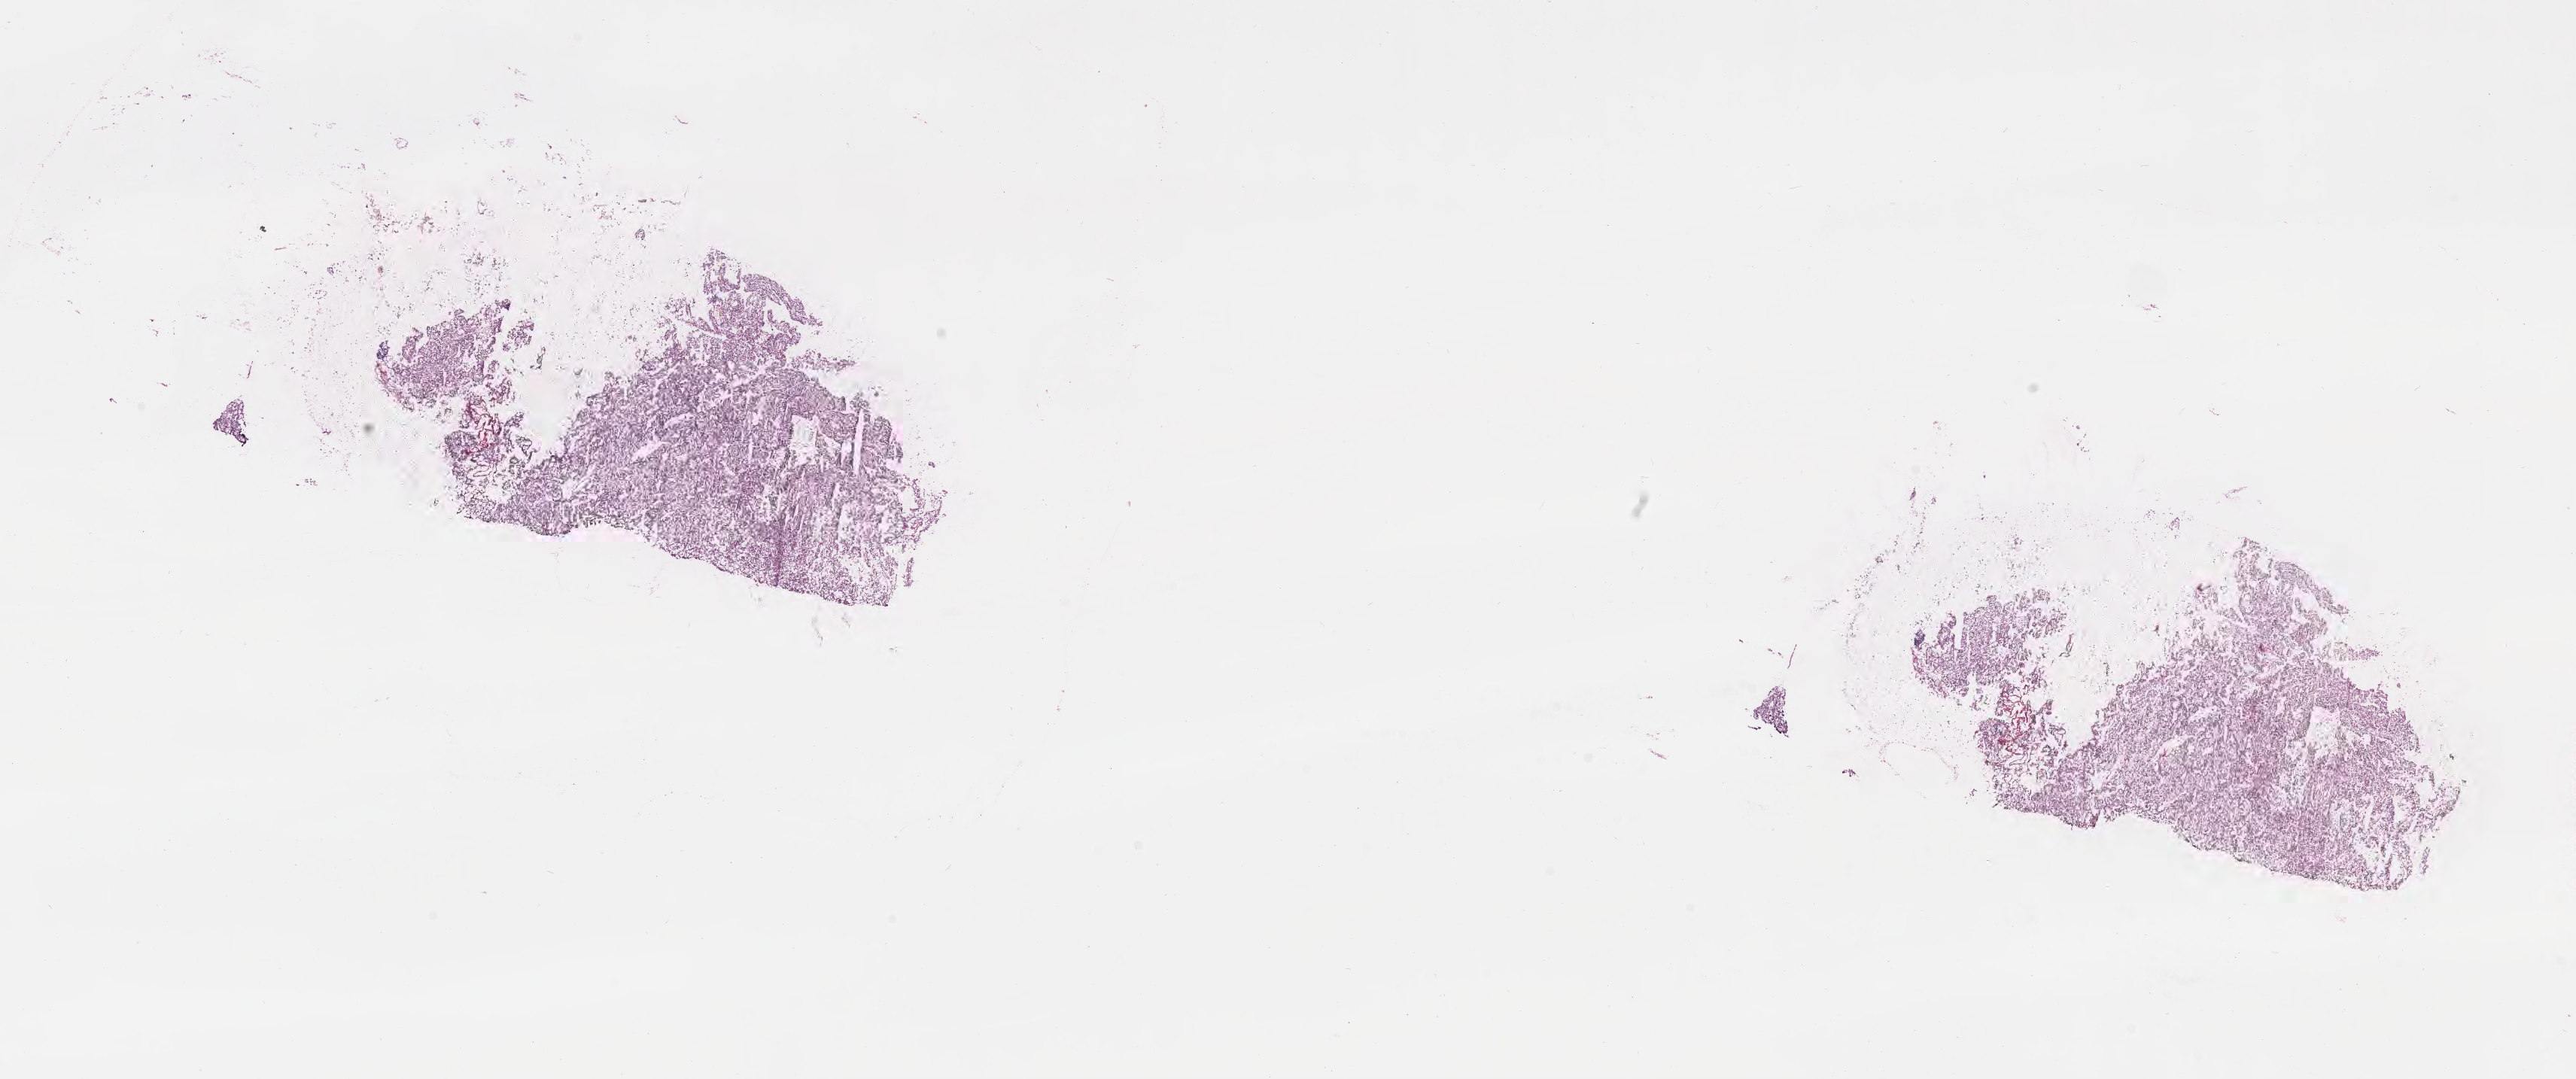
Haematoxylin and eosin whole-slide image, shown as a low-resolution overview of the whole scanned area (about 27.7 x 11.6 mm); frozen section; primary tumor; site: kidney. Female, age 47 years at initial diagnosis. Tumor grade: G2 (moderately differentiated). Composition of this section per pathologist review: tumor cells 100%, tumor nuclei 98%, stromal cells 0%, necrosis 0%, normal cells 0%. Inflammatory infiltration, as recorded: lymphocyte infiltration 0%, monocyte infiltration 0%, neutrophil infiltration 0%.
- section: bottom of the tissue portion
- histologic diagnosis: Renal cell carcinoma, NOS
- AJCC pathologic stage: Stage III